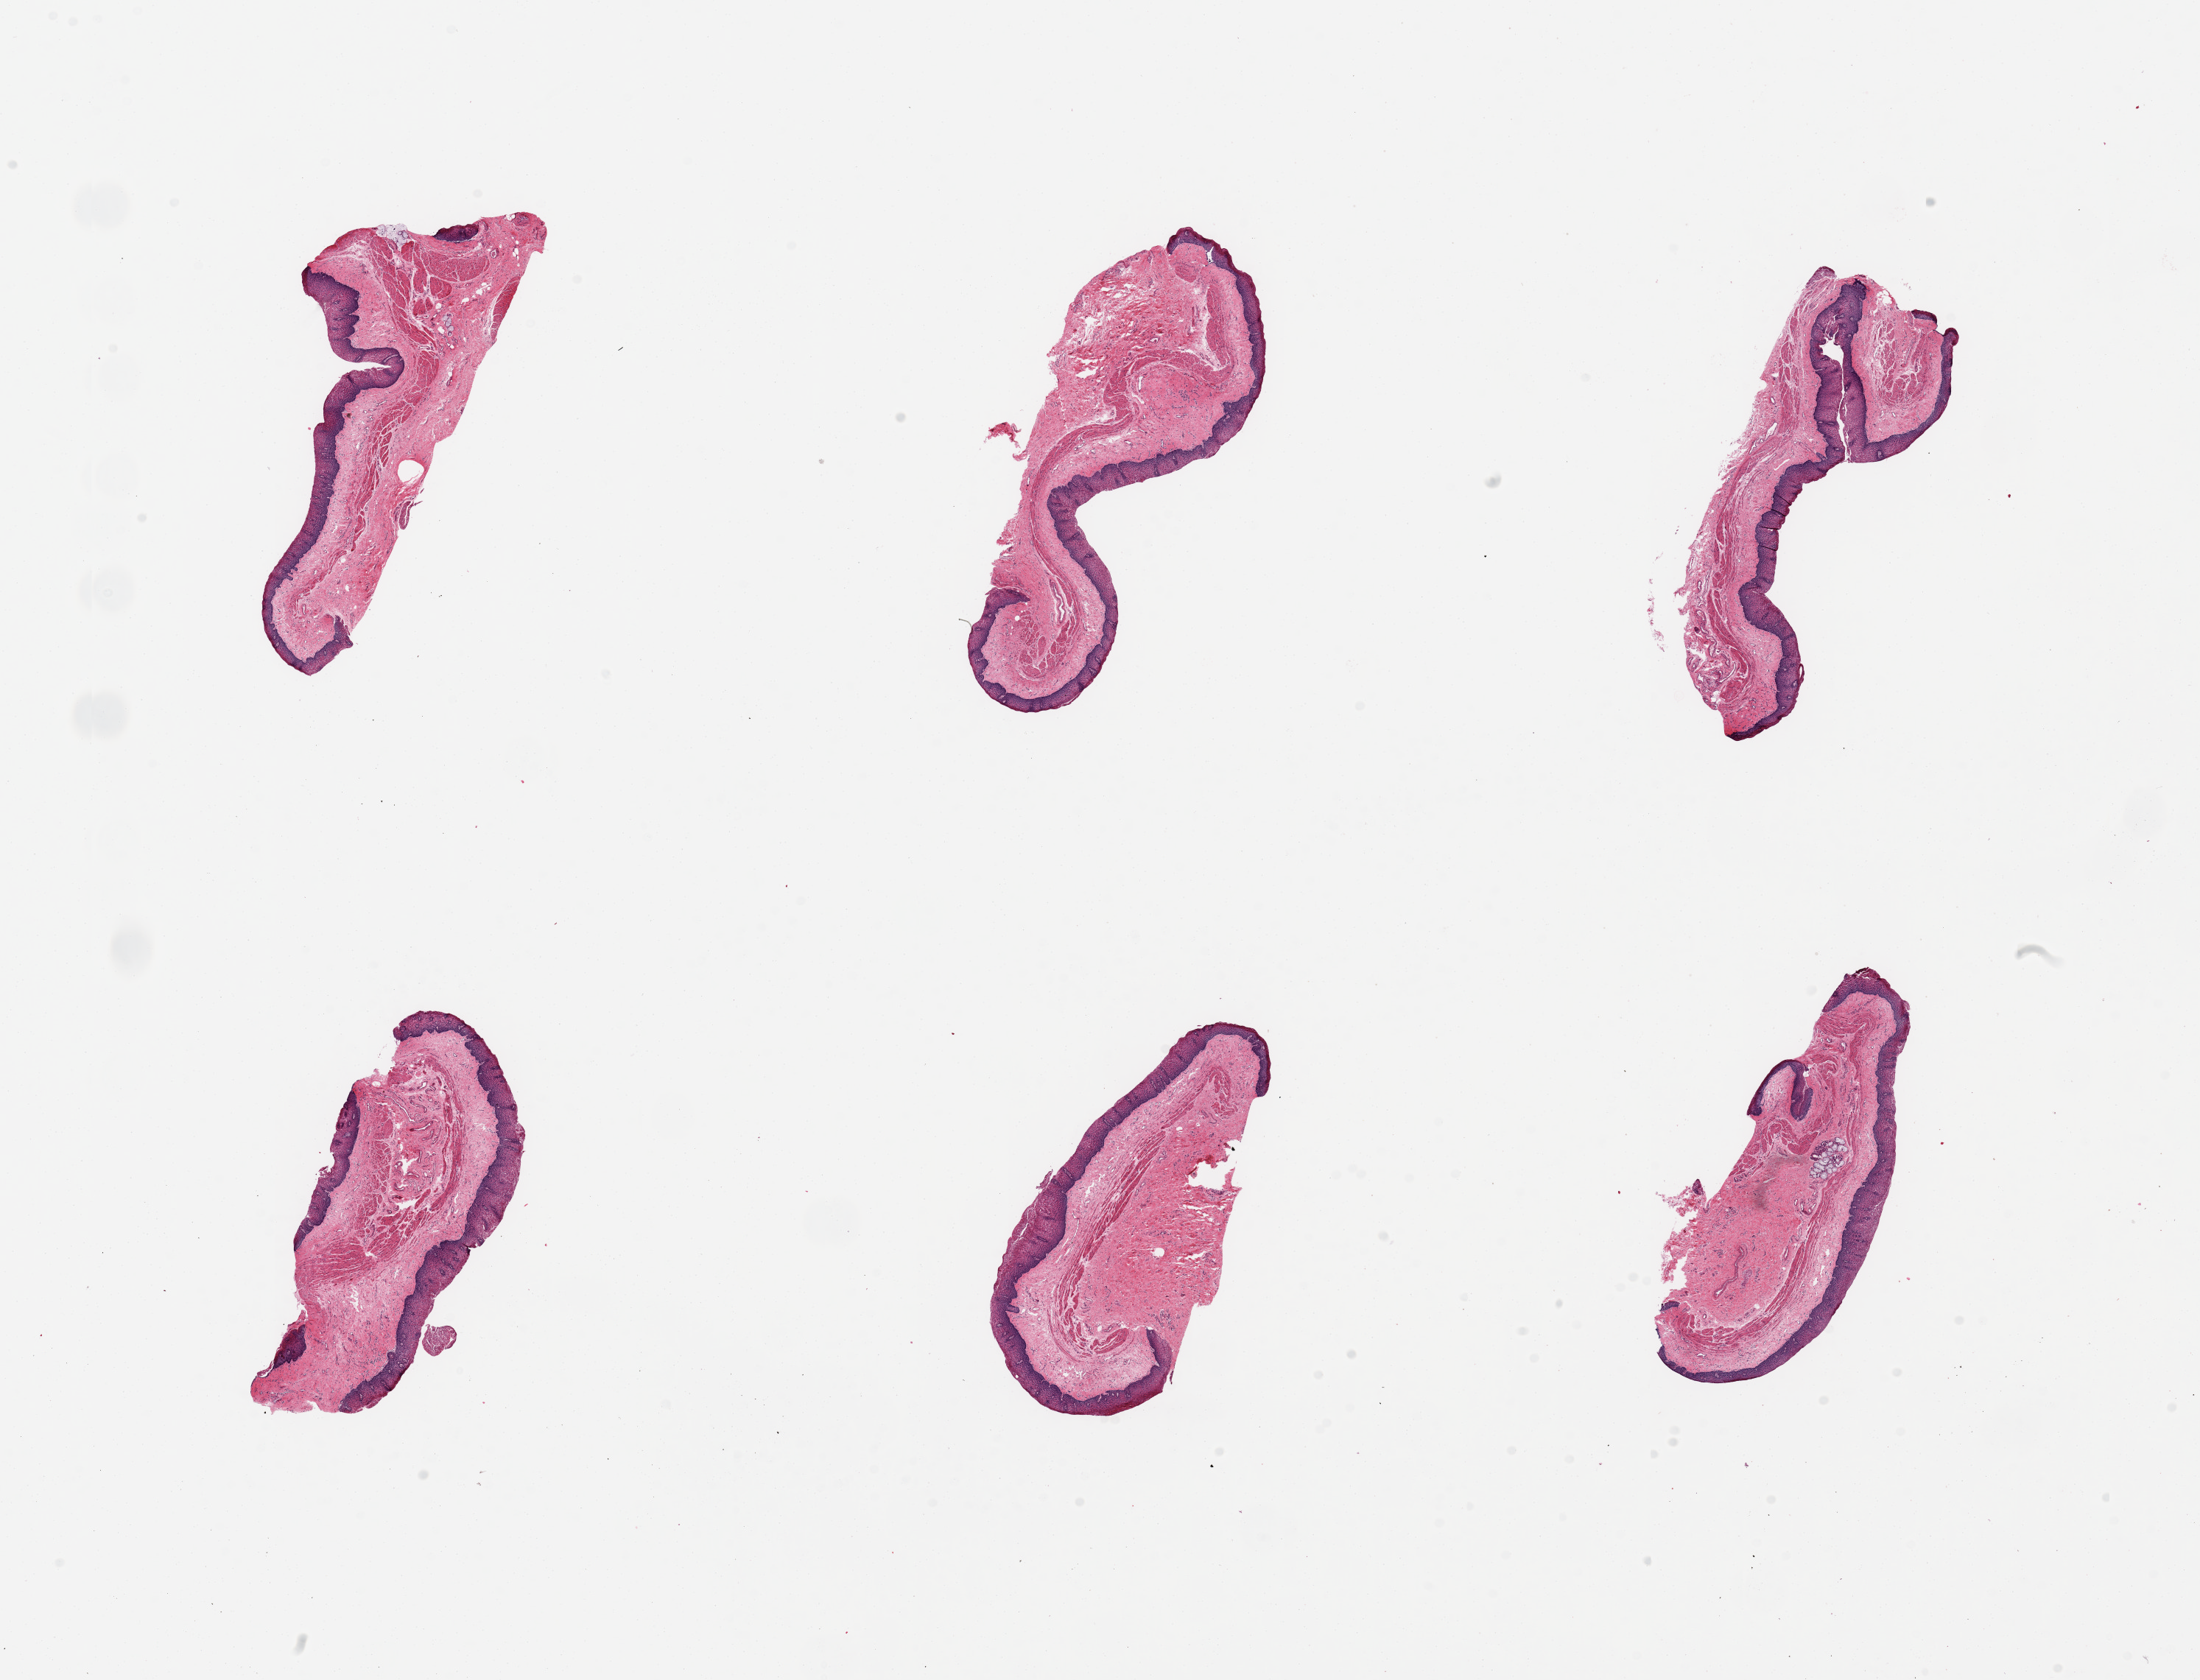
Whole-slide image, H&E stain — whole scanned area (about 23.6 x 18.0 mm) shown as a low-resolution overview, PAXgene-fixed paraffin-embedded (PFPE) section, sampled site (target tissue): esophageal mucous membrane, donor tissue sample. Donor sex: female.
Review note (as recorded): 6 pieces; well preserved mucosa with scattered submucosal glands.